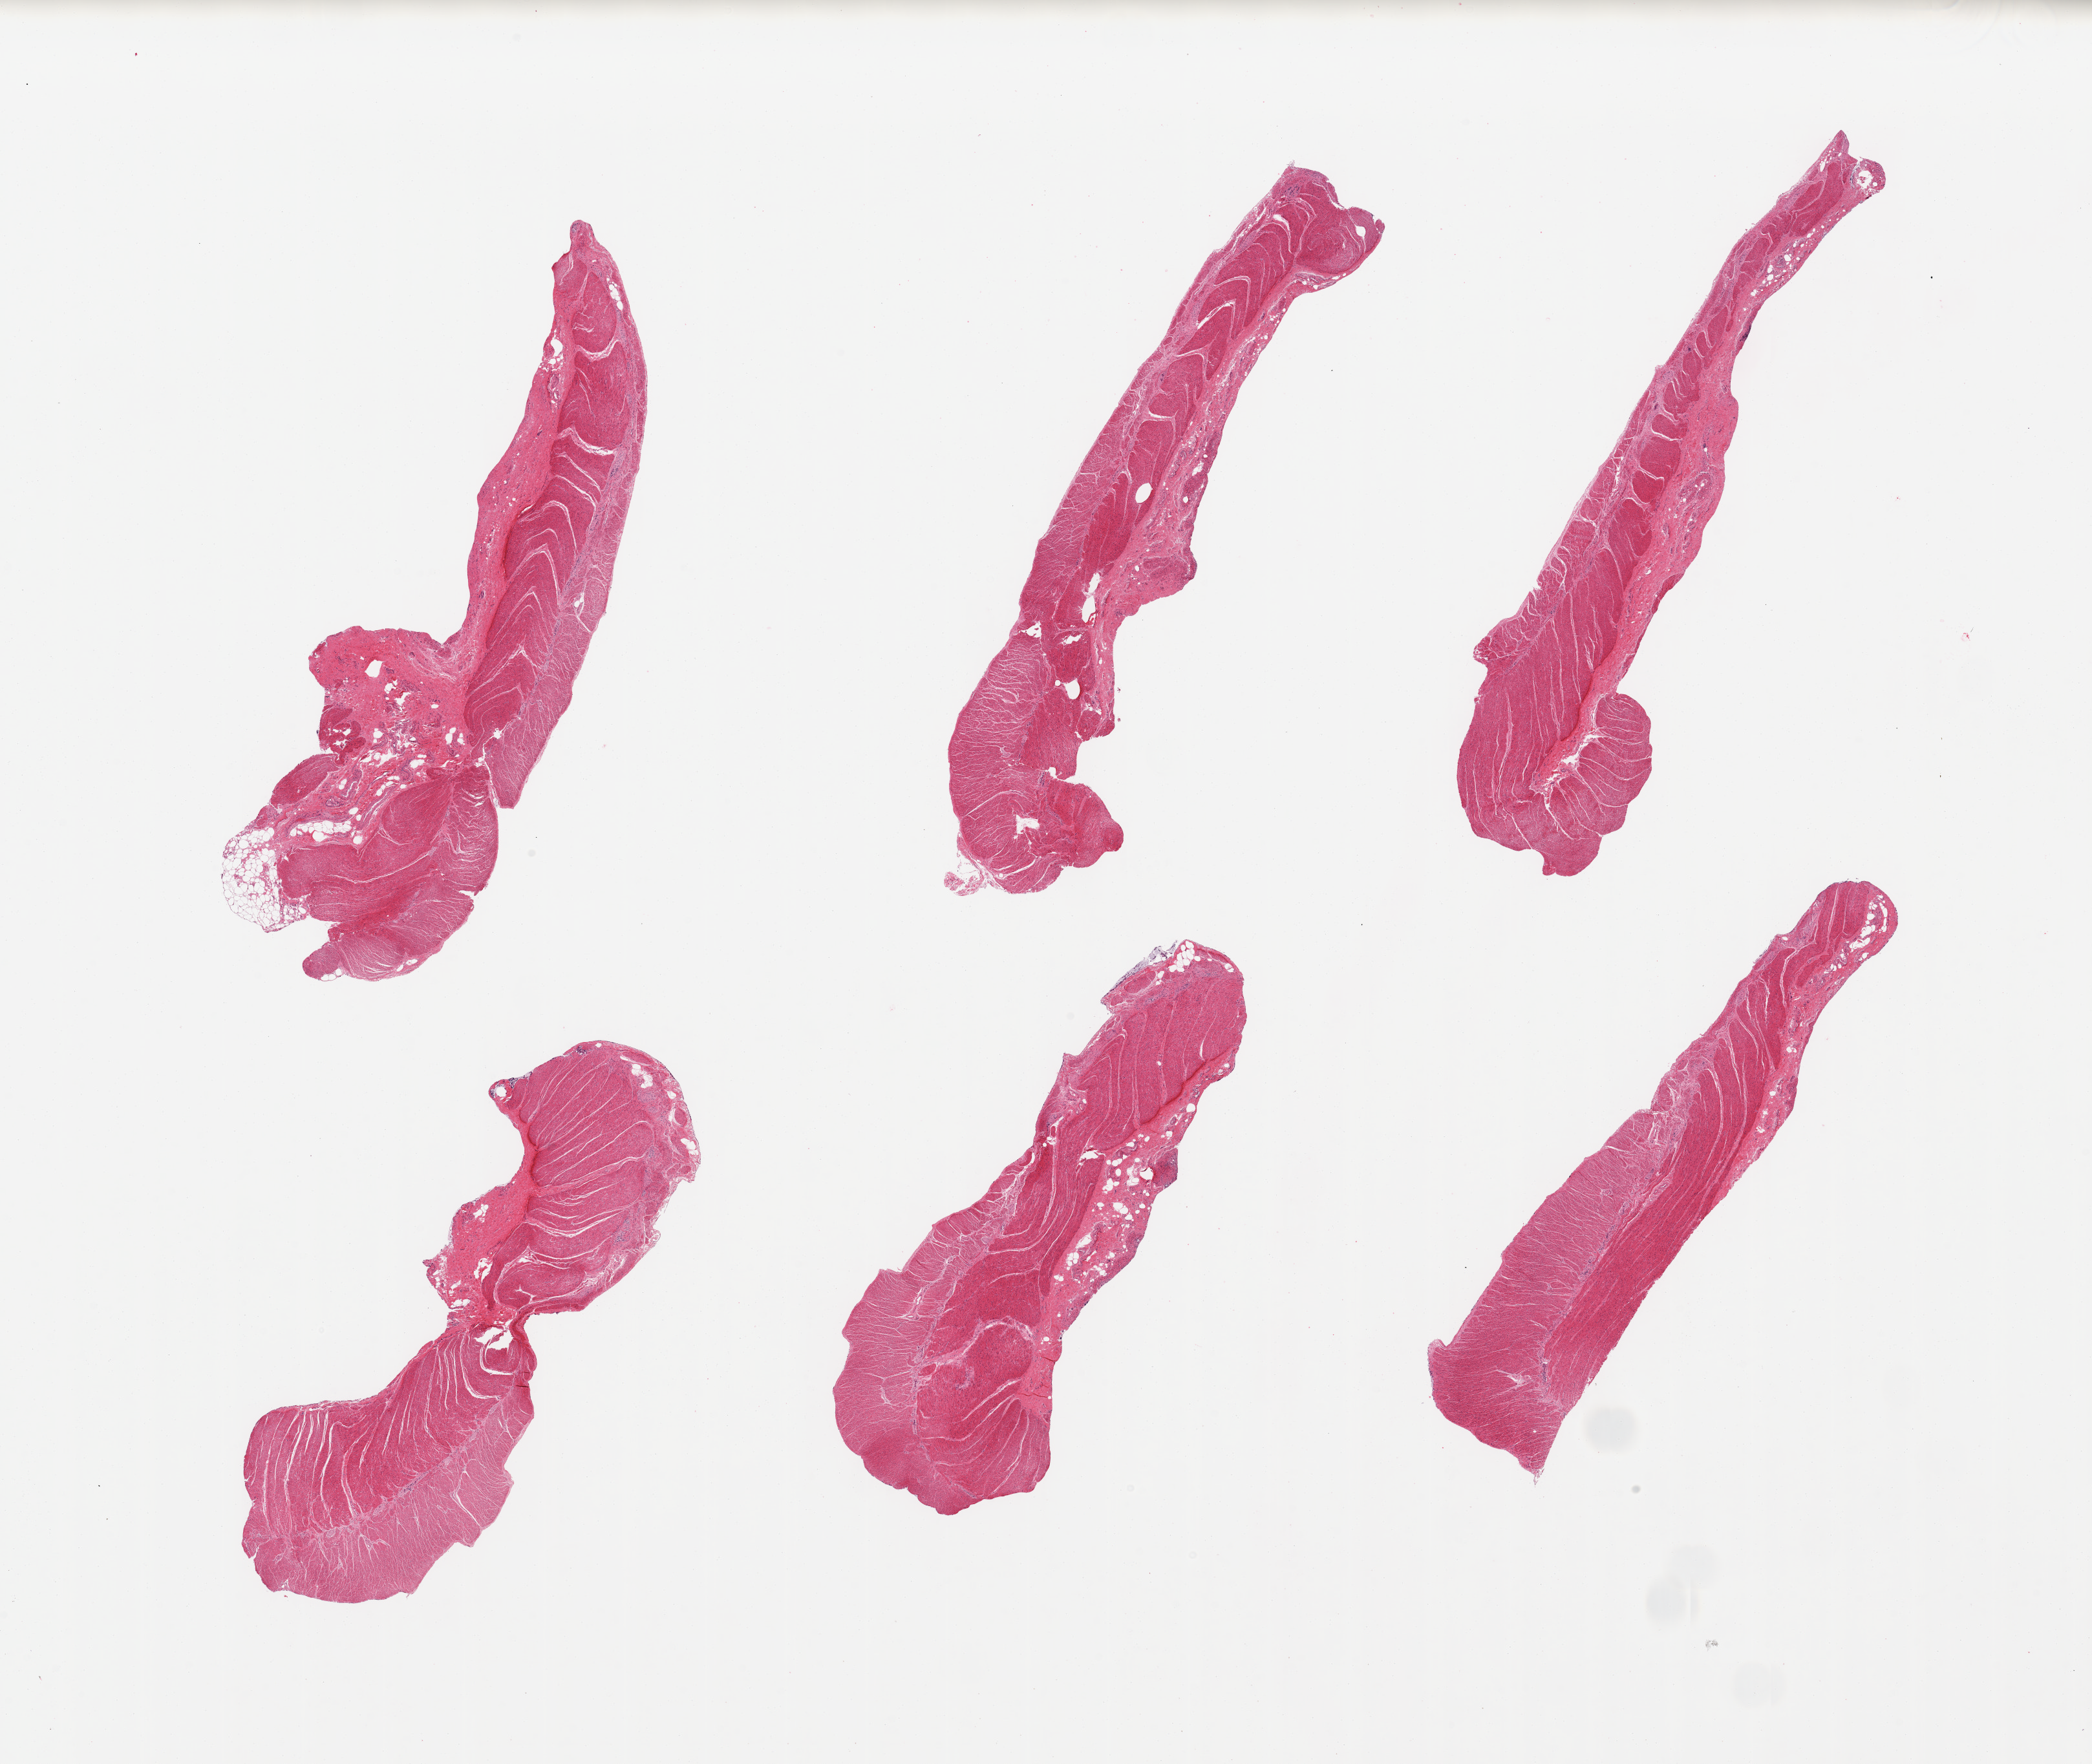
Digitized H&E-stained section, brightfield, low-resolution overview of the scanned area, about 25.6 x 21.6 mm (slide scanned at 20x). PAXgene-fixed, paraffin-embedded tissue. Target tissue: sigmoid colon. Donor tissue sample.
Review note (as recorded): 6 pieces, confirmed target muscularis.